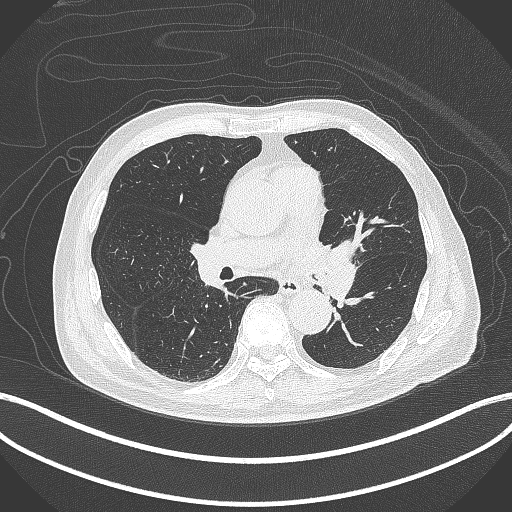
Chest CT, one axial slice; 120 kVp; lung window (W 1500 / L -600 HU); 1 mm slice thickness; 512 × 512 image matrix. Male patient, age 77 years. From the clinical record (not read from this slice): clinical TNM (as recorded): T3 N1 M0.
Annotated regions visible in this slice (rectangle marked by the reading radiologist):
- lung tumour (recorded histology: adenocarcinoma): bounding box [x1, y1, x2, y2] px = [313, 241, 359, 299]